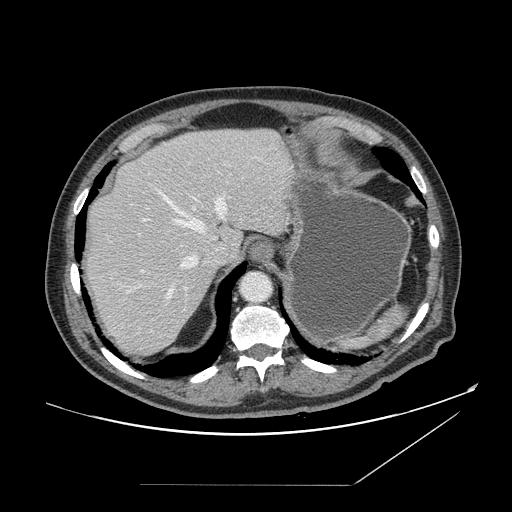
Contrast-enhanced abdominal CT, one axial slice; position 123 of 166 along the scan axis; 120 kVp; soft-tissue window (W 400 / L 40 HU); 2.5 mm slice thickness; 512 × 512 image matrix, field of view 416 × 416 mm. Male patient, age 80 years. From the clinical record (not read from this slice): diagnosis: colorectal cancer liver metastases, imaged before liver resection; multiple liver metastases: no.
Outlined on this slice (expert manual segmentation):
- hepatic veins: bounding box <128,196,227,301> (left, top, right, bottom; pixels)
- liver: <84,129,292,356>
- planned liver remnant (the part of the liver to remain after resection): <86,129,292,256>
- portal vein (with intrahepatic branches): <140,207,196,273>